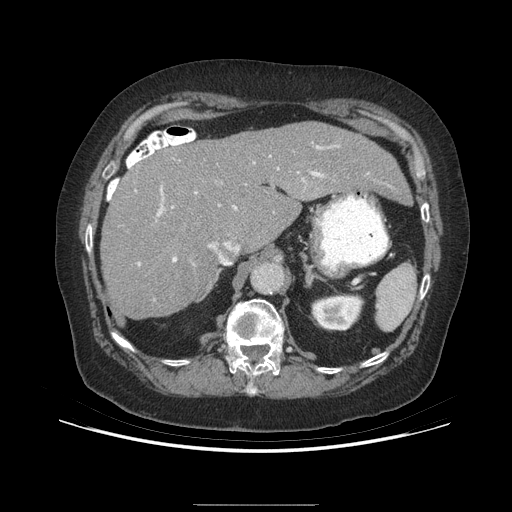
Contrast-enhanced abdominal CT (liver protocol), one axial slice; slice 162 of 192 in the series (ordered by position); reconstruction kernel STANDARD; 140 kVp; soft-tissue window (W 400 / L 40 HU); 2.5 mm slice thickness; 512 × 512 image matrix. Case-level facts recorded for this patient, not image findings: diagnosis: hepatocellular carcinoma (patient treated with transarterial chemoembolisation; whether this scan precedes or follows treatment is not stated here); TNM stage (as recorded): Stage-I; Child-Pugh class: A; tumour differentiation: moderately differentiated; tumour nodularity: uninodular.
Annotated regions visible in this slice (semi-automatic segmentation, software-assisted and operator-edited):
- liver parenchyma outside the tumour (the mass and vessels are separate outlines, so this box may not span the whole liver): box from (x=100, y=122) to (x=408, y=318) px
- liver vessels: (x=138, y=145)–(x=337, y=266)